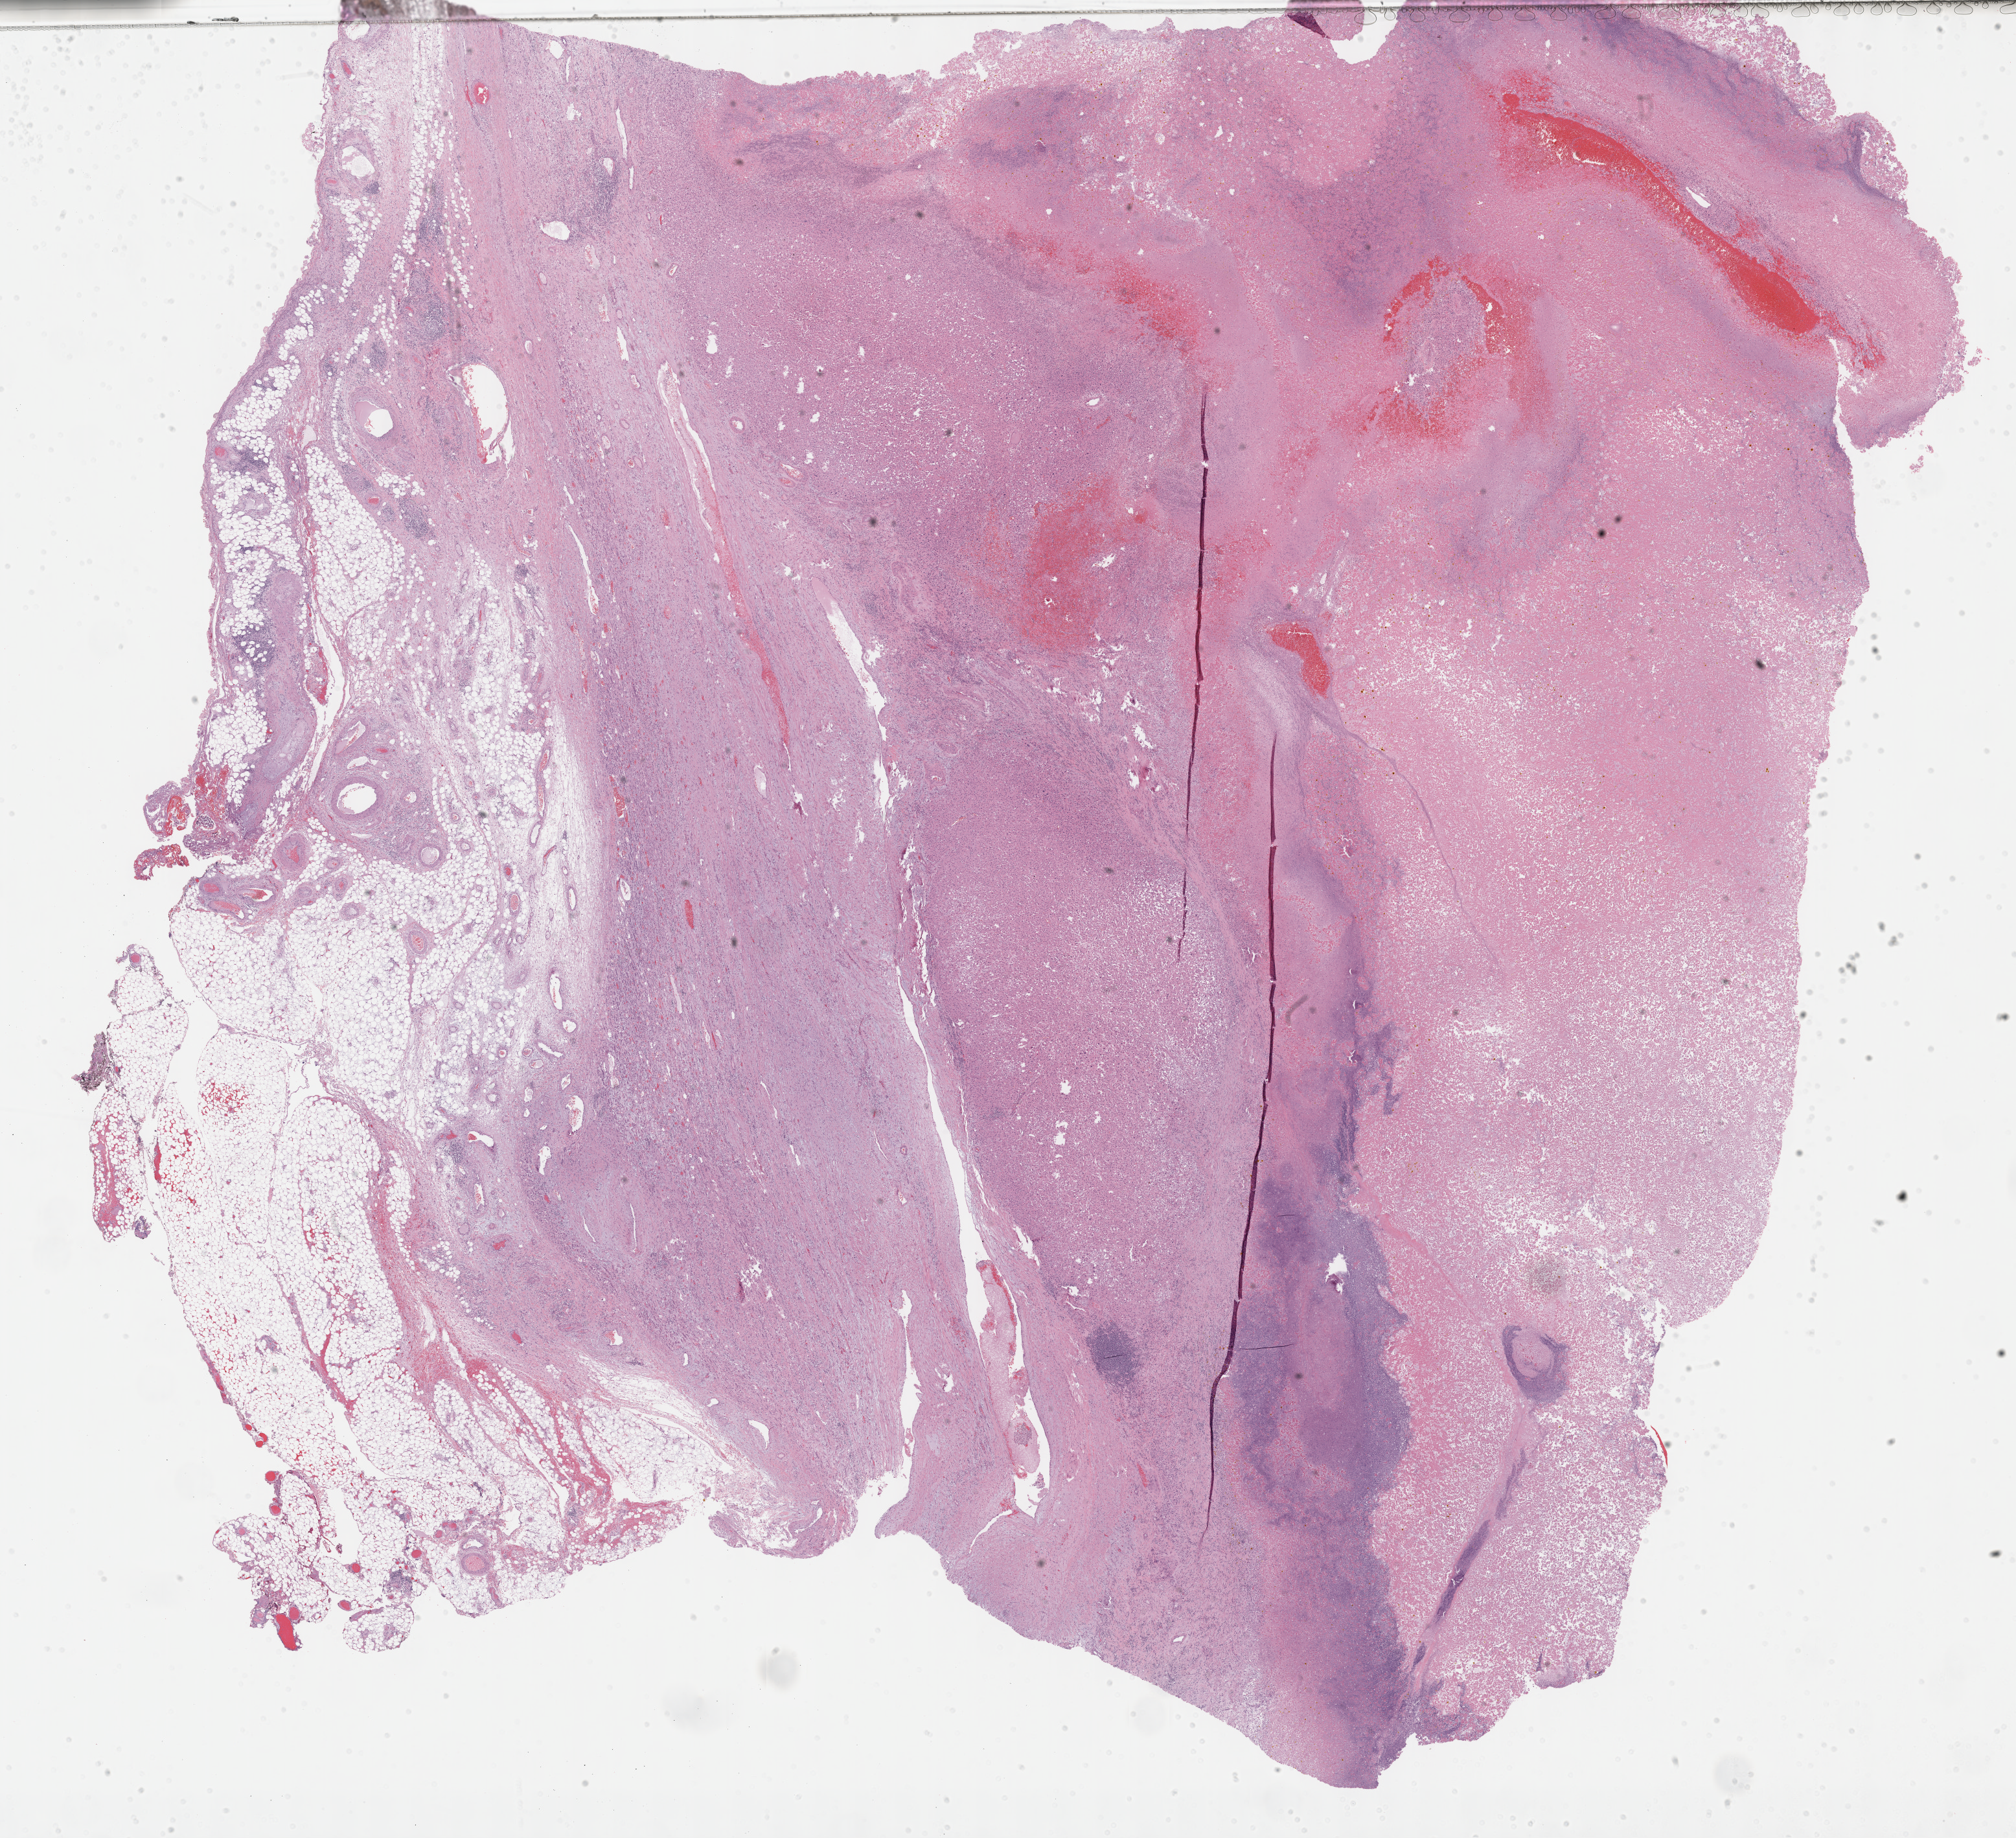
Whole-slide histology image, H&E — whole scanned area (about 25.2 x 22.9 mm, acquisition: 40x scan) shown as a low-resolution overview. Formalin-fixed paraffin-embedded (FFPE) diagnostic section. Primary tumour sample from the adrenal cortex. Patient: female, age at initial diagnosis 65 years.
Pathologic diagnosis: Adrenal cortical carcinoma (cortex of adrenal gland). Lymph nodes positive (case pathology): 0 of 17 examined.